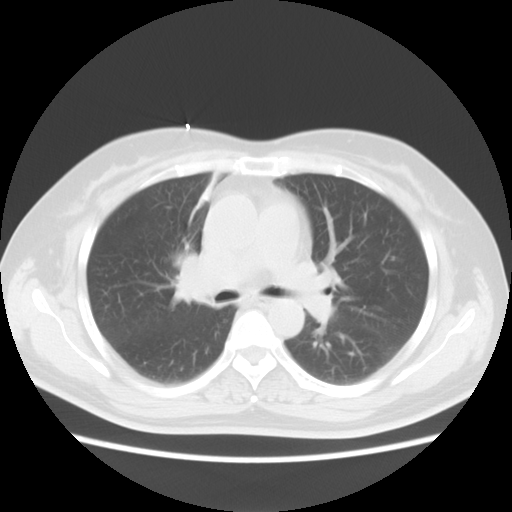
Chest CT, one axial slice; slice 5 of 18 in the series (ordered by position); lung window (W 1500 / L -600 HU); 5 mm slice thickness; 512 × 512 image matrix, field of view 350 × 350 mm. Patient: female, 54 years. Case-level facts recorded for this patient, not image findings: clinical TNM (as recorded): T2 N3 M0; histopathological grade: G3.
Annotated regions visible in this slice (bounding box drawn by a radiologist):
- lung tumour (recorded histology: small cell carcinoma): bounding box [x1, y1, x2, y2] px = [161, 244, 198, 306]